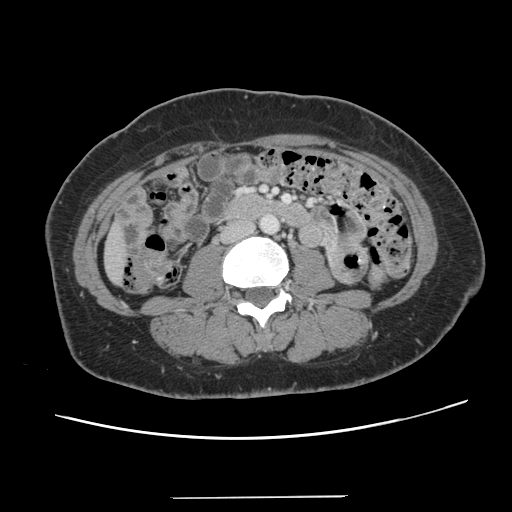
Contrast-enhanced abdominal CT, one axial slice. Slice 20 of 141 in the series (ordered by position). 120 kVp. Intravenous contrast given. Soft-tissue window (W 400 / L 40 HU). 2.5 mm slice thickness. 512 × 512 image matrix, field of view 366 × 366 mm. Female patient, age 53 years. Case-level facts recorded for this patient, not image findings: diagnosis: colorectal cancer liver metastases, imaged before liver resection; multiple liver metastases: no; largest metastasis: 14.5 cm; disease in both lobes: yes.
Structures marked on this image (manually delineated by an expert):
- liver: box from (x=106, y=226) to (x=127, y=282) px
- planned liver remnant (the part of the liver to remain after resection): (x=106, y=227)–(x=127, y=282)